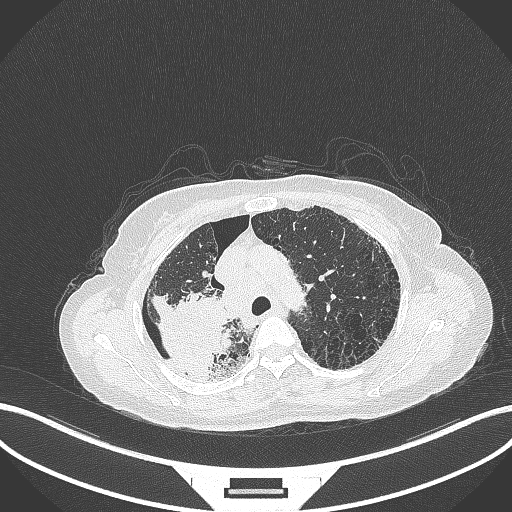
Chest CT, one axial slice; slice 261 of 408 in the series (ordered by position); reconstruction kernel B70f; 120 kVp; lung window (W 1500 / L -600 HU); 1 mm slice thickness; 512 × 512 image matrix. Female patient, age 64 years. Case-level facts recorded for this patient, not image findings: clinical TNM (as recorded): T3 N3 M0.
Structures marked on this image (bounding box drawn by a radiologist):
- lung tumour (recorded histology: squamous cell carcinoma): box from (x=147, y=289) to (x=230, y=378) px